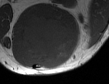
MRI of an extremity soft-tissue mass, one axial slice. Slice 34 of 50 in the series (ordered by position). MR volume resampled by the dataset authors to the PET/CT grid (not the native acquisition matrix). 3.27 mm slice thickness. 109 × 84 image matrix, field of view 106 × 82 mm. Male patient. Case-level facts recorded for this patient, not image findings: histological type: synovial sarcoma; site of the primary tumour: left poplietal fossa.
Outlined on this slice (expert contour drawn on MRI and transferred to this co-registered scan by the dataset authors):
- gross tumour volume (mass): bounding box [x1, y1, x2, y2] px = [21, 16, 74, 65]